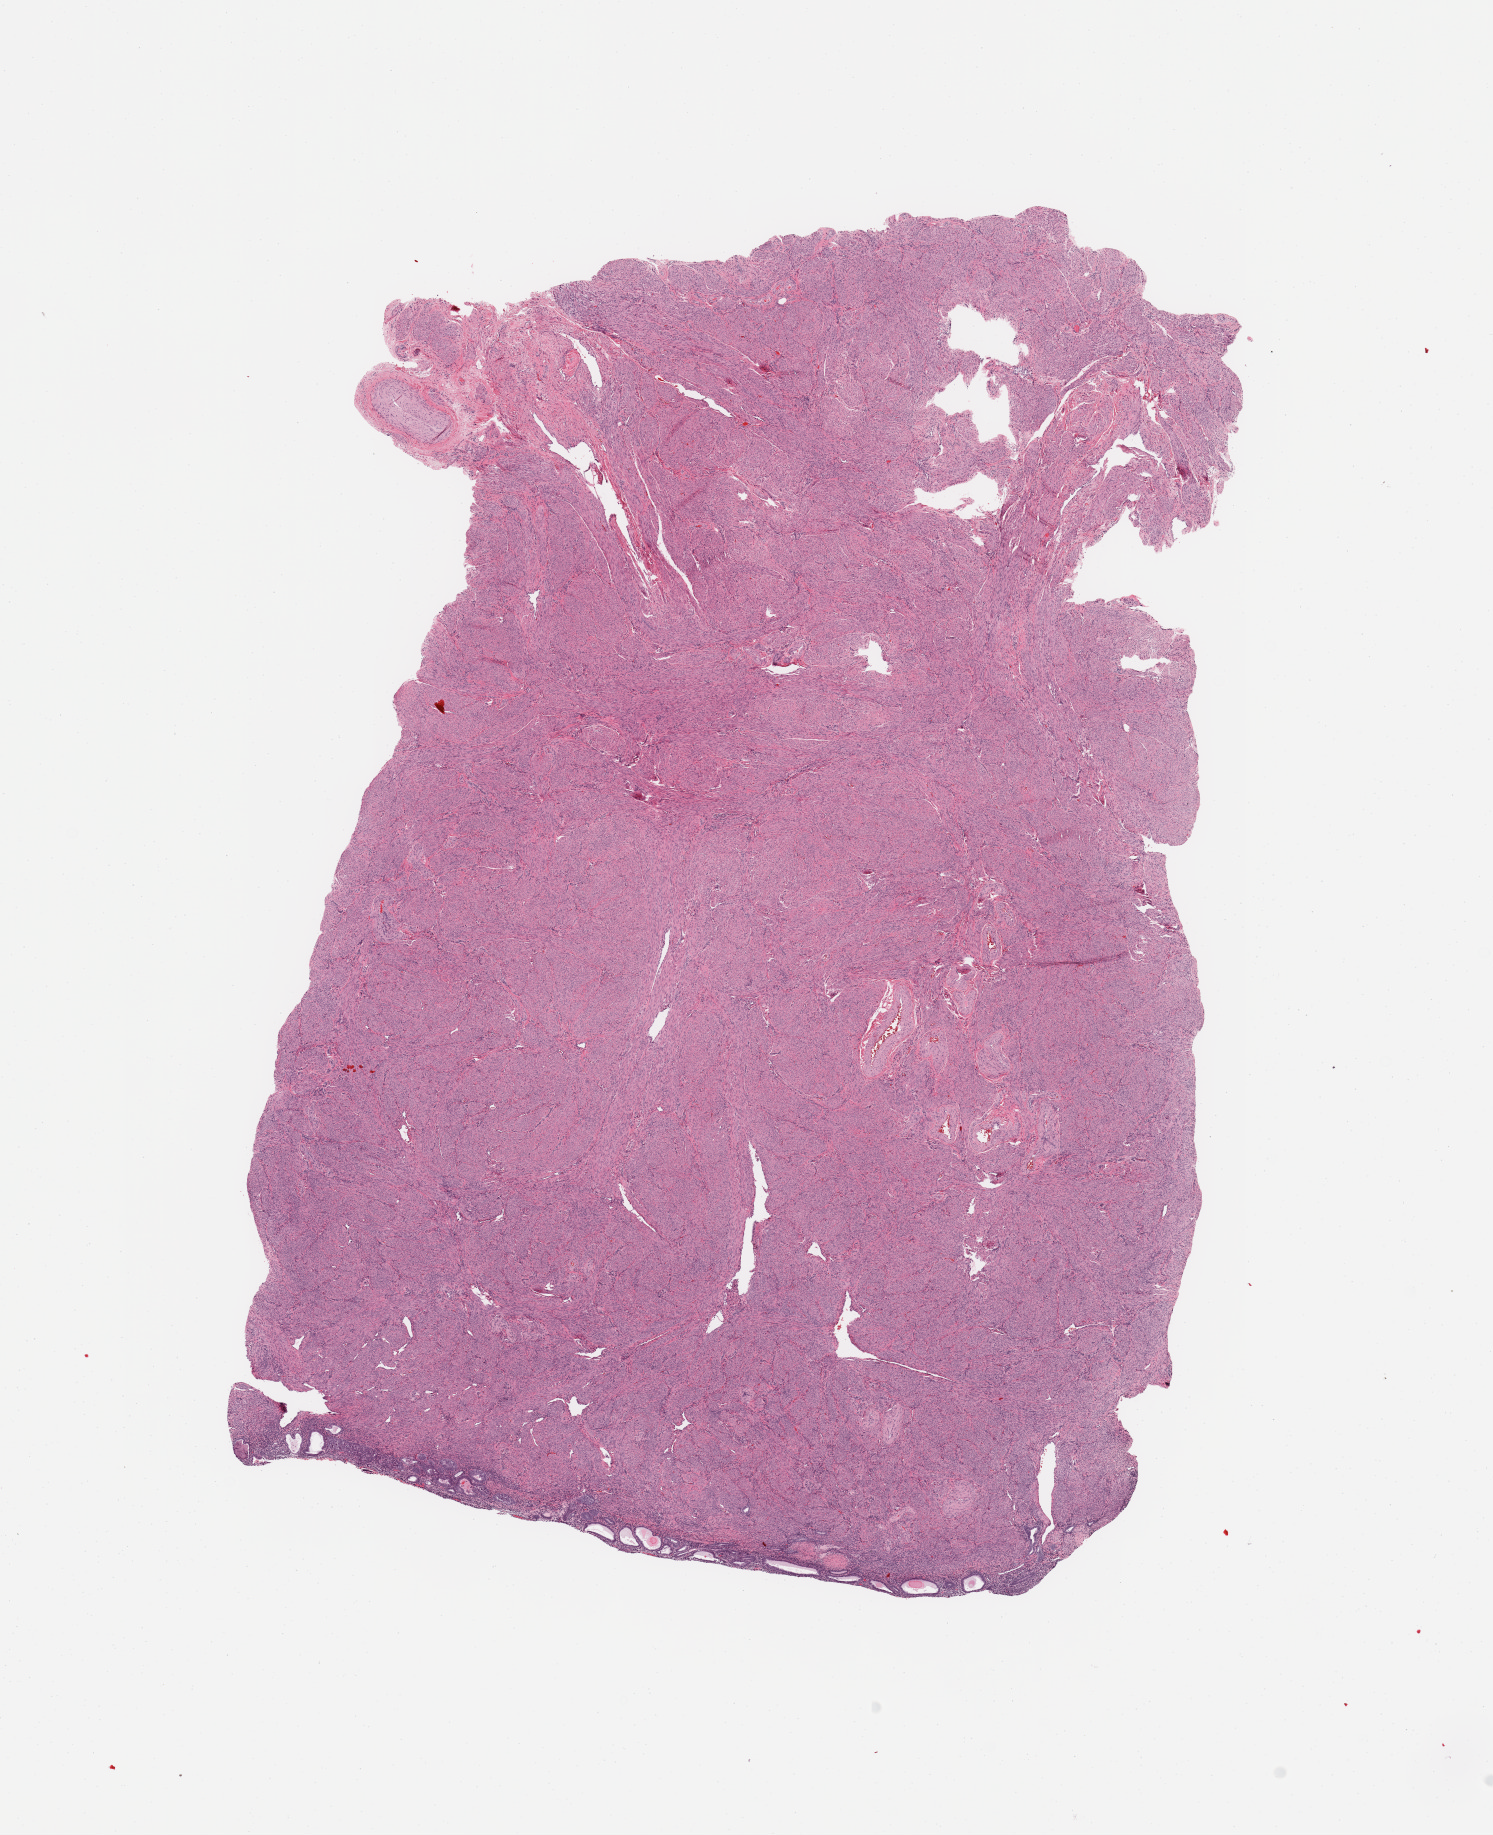
Digitized H&E-stained tissue section (whole slide) — a low-resolution overview of the entire scanned area, about 11.8 x 14.5 mm (slide scanned at 20x). Normal (non-tumour) tissue sample, sampled site: uterus. 57-year-old female patient.
This section: normal (non-tumour) tissue from the same patient. Patient diagnosis: Endometrioid adenocarcinoma, NOS.